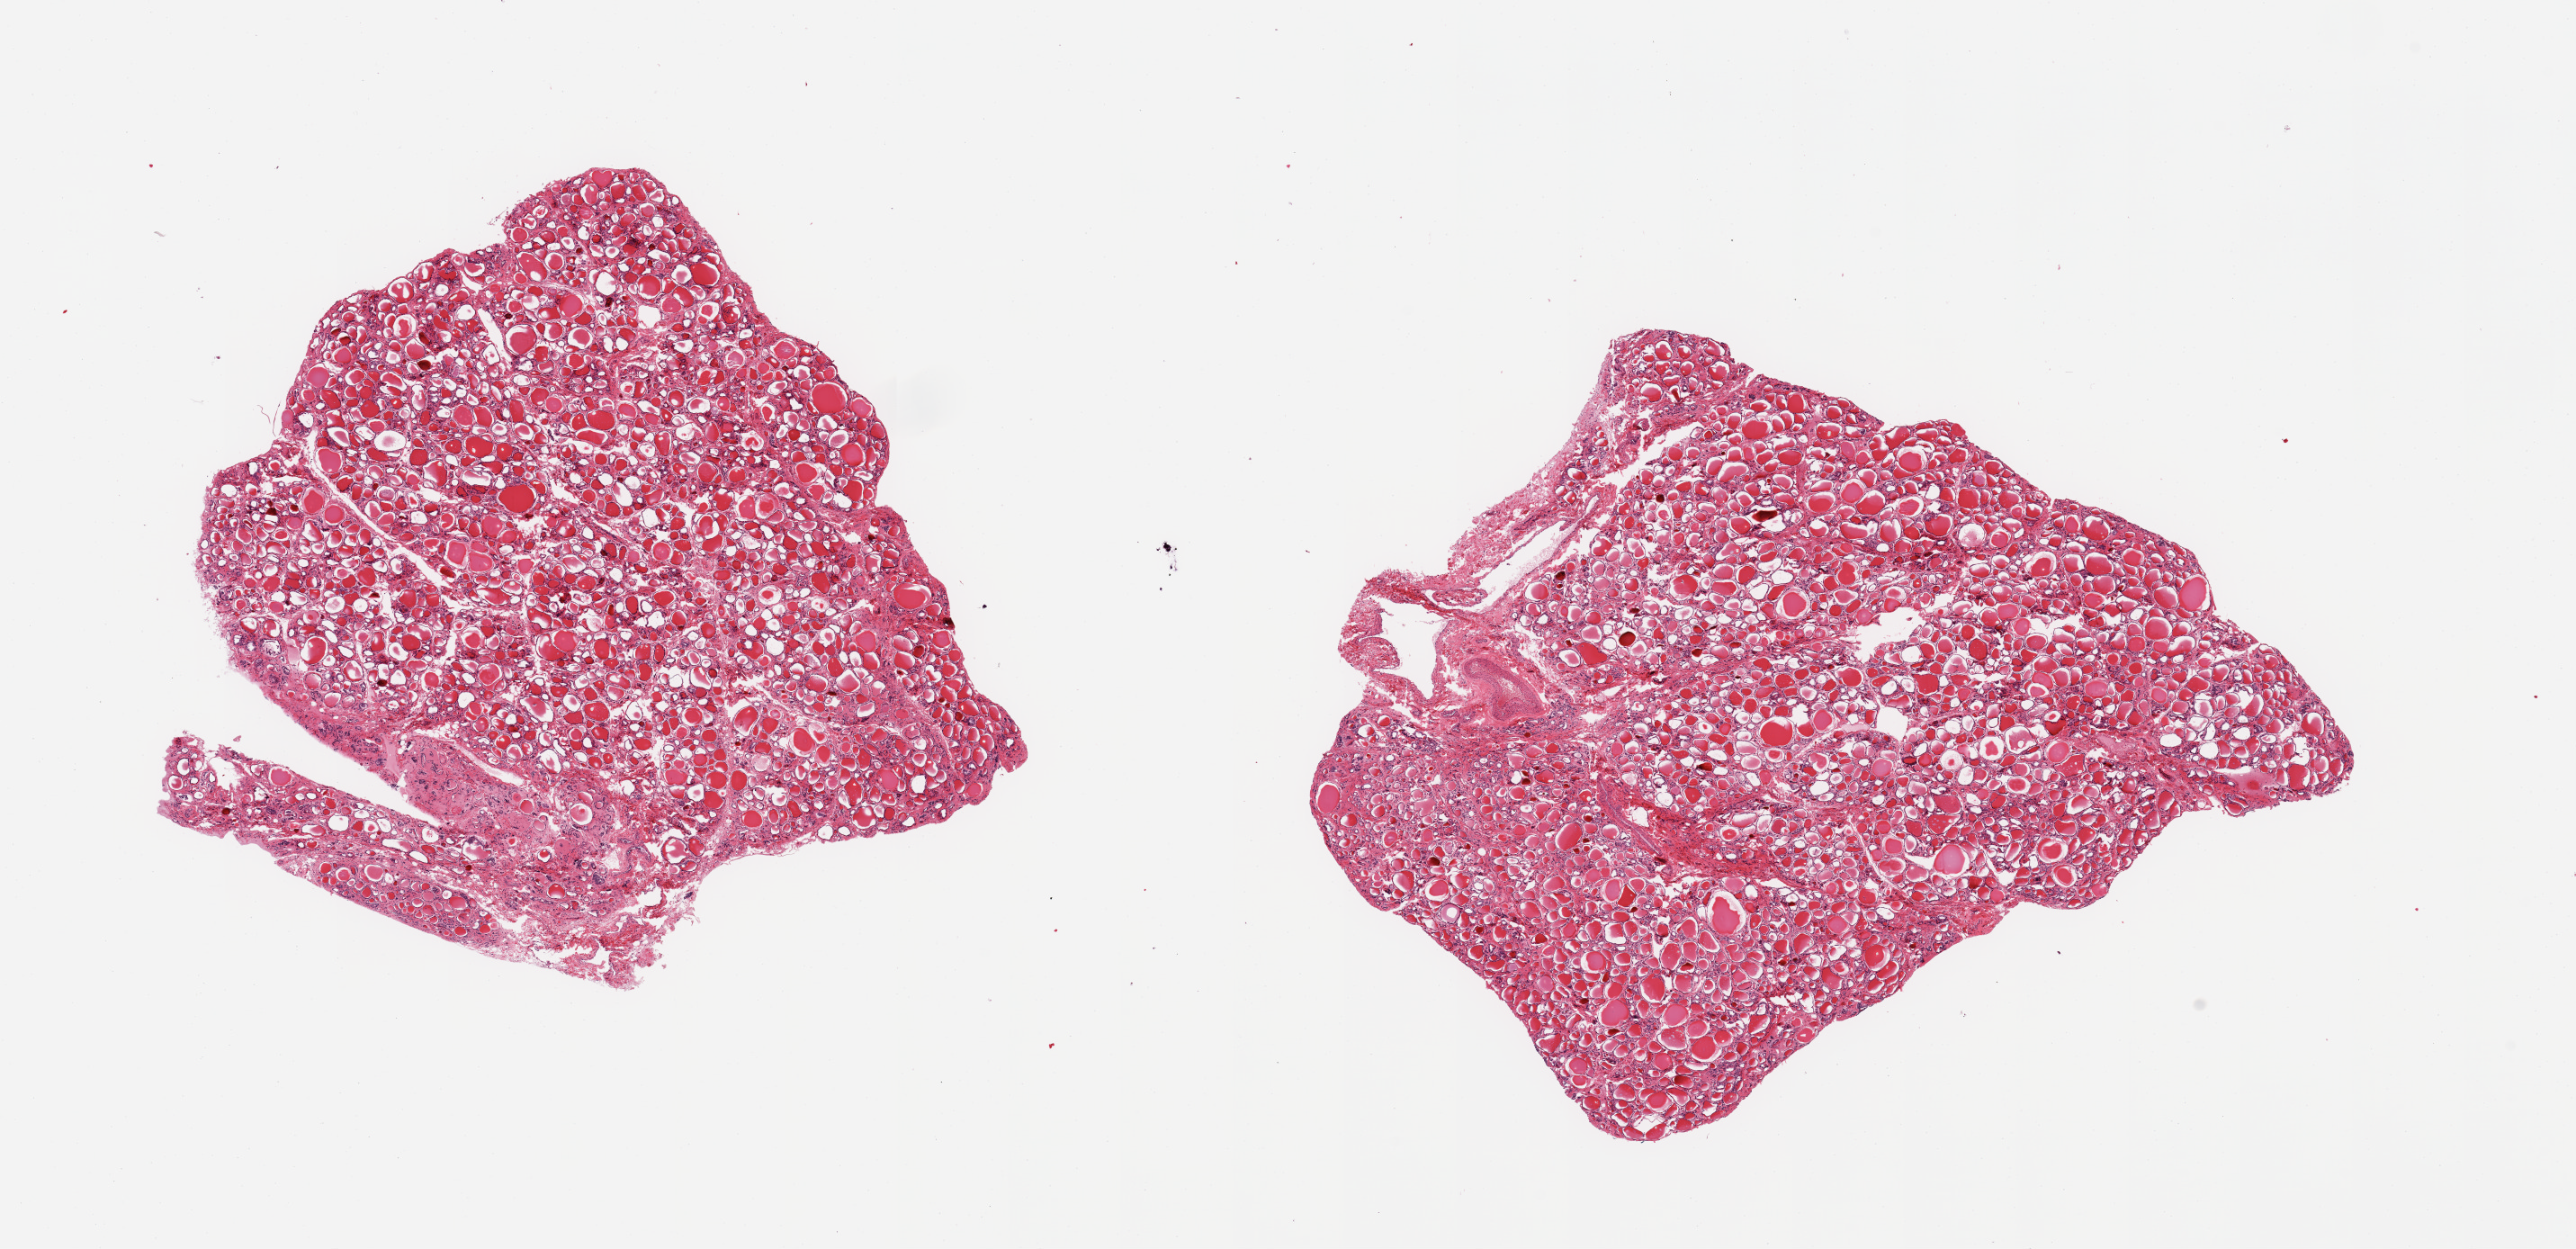
Haematoxylin and eosin whole-slide image, whole scanned area (about 22.6 x 11.0 mm, acquisition: 20x scan) shown as a low-resolution overview, PAXgene-fixed, paraffin-embedded tissue, target tissue: thyroid, tissue donor sample. Male donor.
Review note (as recorded): 2 pieces, no abnormalities.